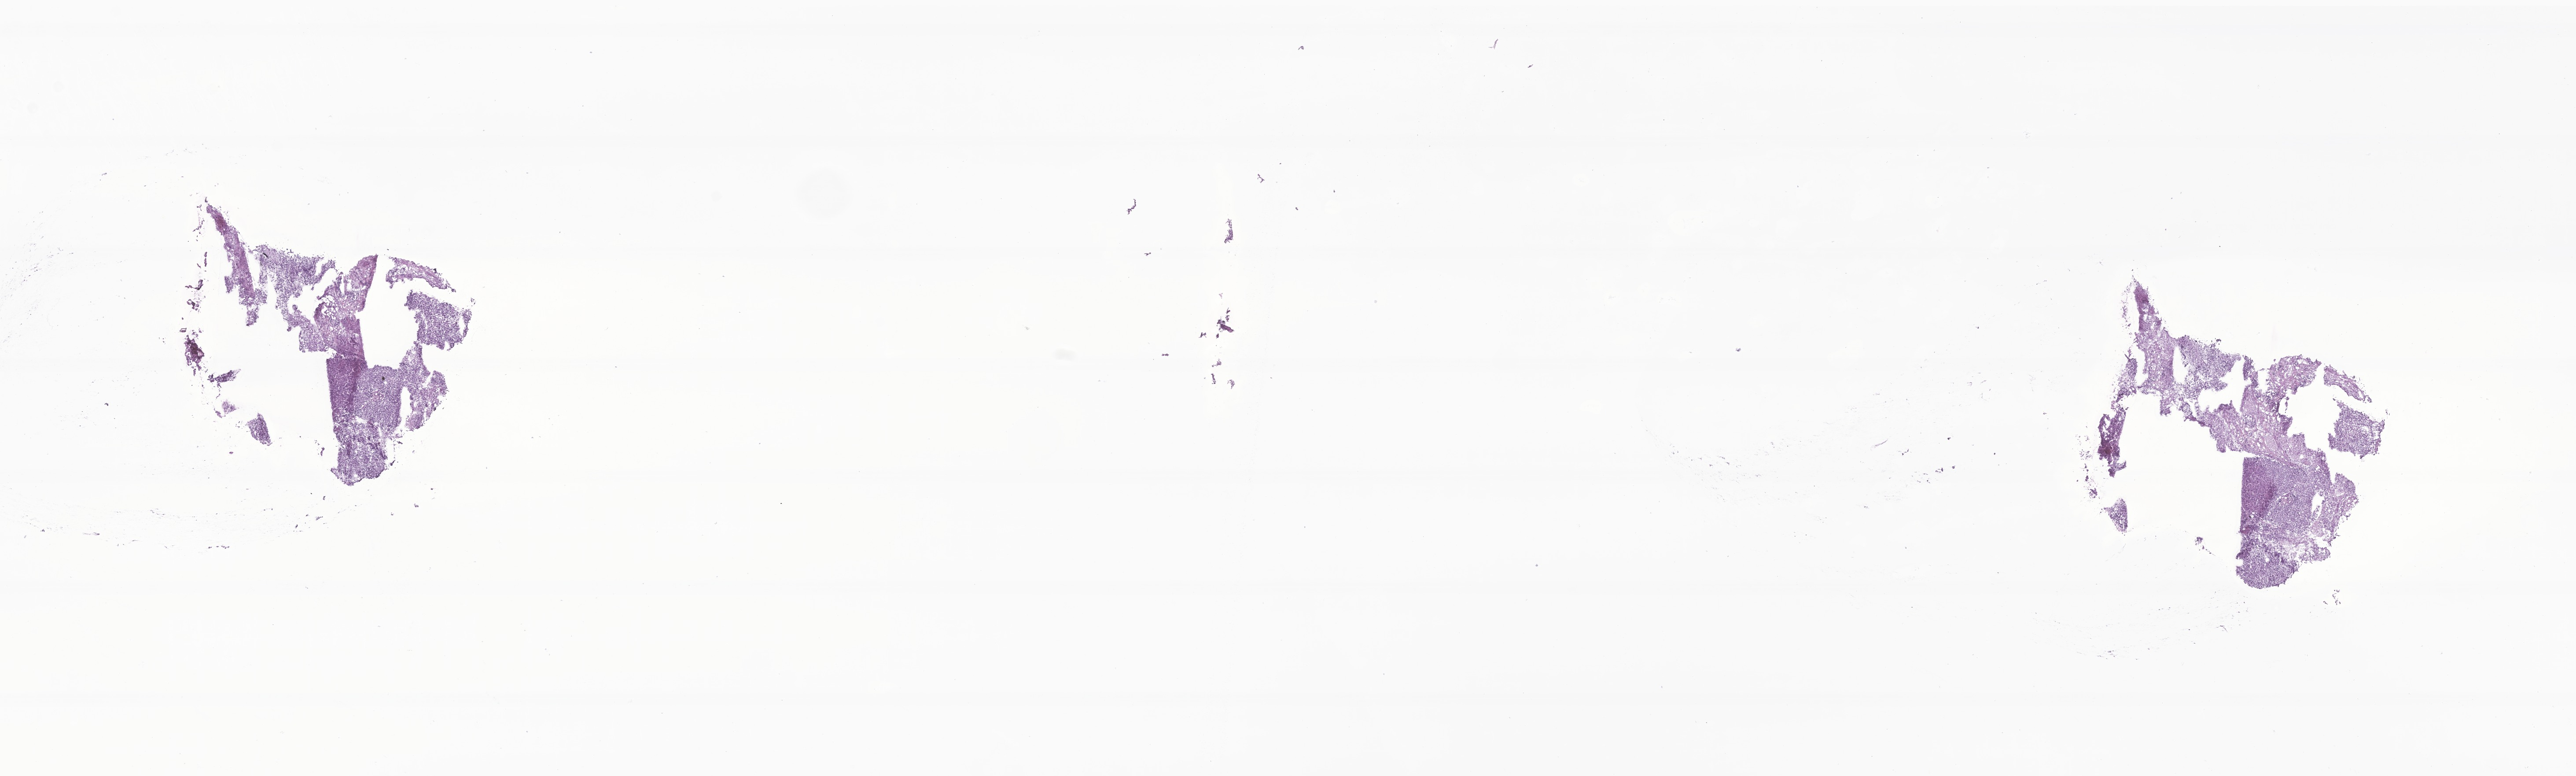
Whole-slide image, H&E stain of tumor tissue from the adrenal gland — a low-resolution overview of the entire scanned area, about 24.7 x 7.4 mm. Frozen section. Patient: male, age 263 days.
• diagnosis (ICD-O-3 morphology term): Ganglioneuroblastoma